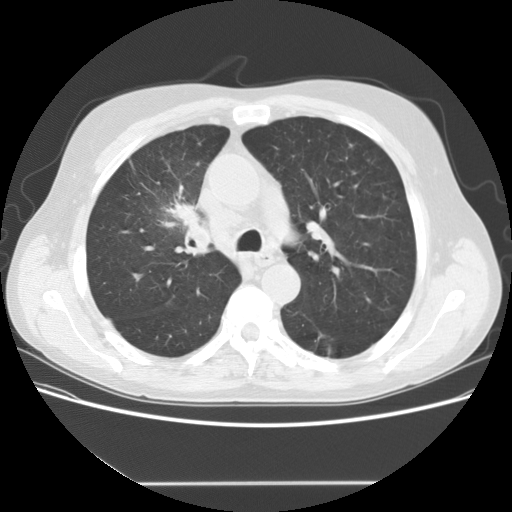
Low-dose screening chest CT, one axial slice. Position 105 of 153 along the scan axis. Reconstruction kernel STANDARD. Lung window (W 1500 / L -600 HU). 2.5 mm slice thickness. 512 × 512 image matrix, field of view 360 × 360 mm.
Annotated regions visible in this slice (outlined manually by an expert reader):
- lesion 1 (tumor, upper lobe of right lung): bounding box <164,199,198,225> (left, top, right, bottom; pixels)